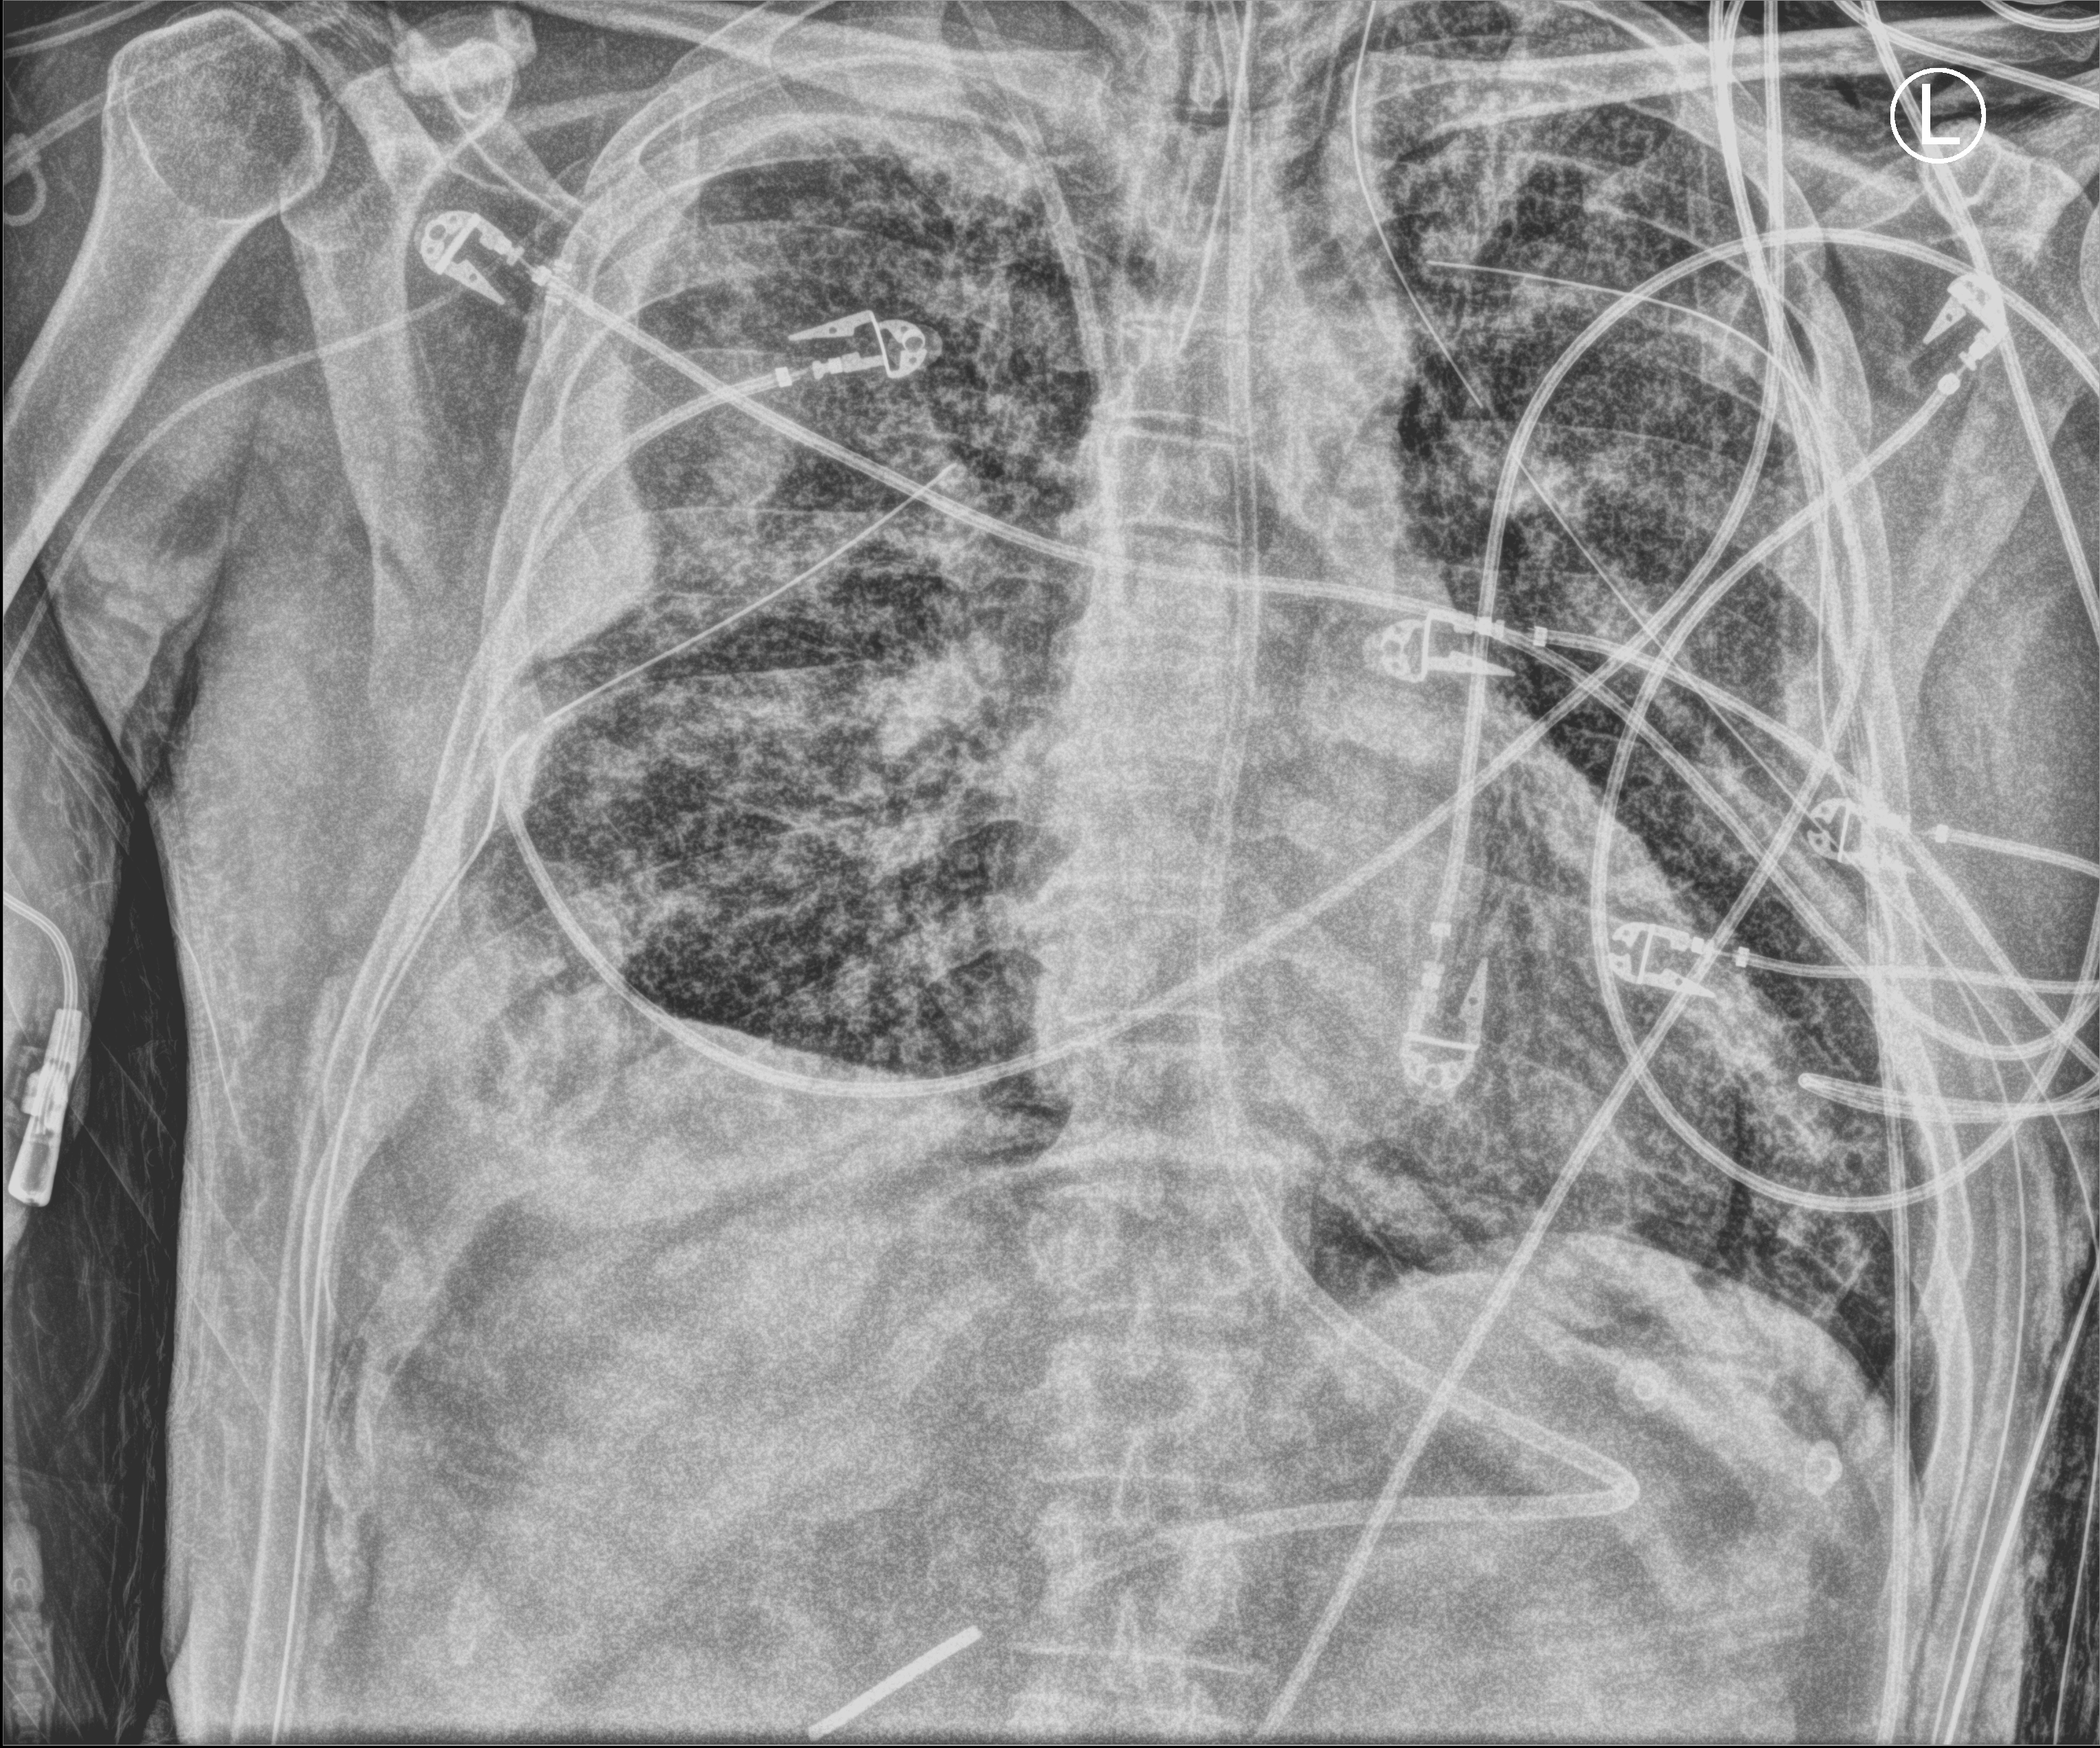
Chest X-ray (portable), anteroposterior (AP) projection. Male patient hospitalised with COVID-19, age 18–59 years.
From the hospital-stay record, not from the radiograph (when in the stay this image was taken is not recorded): COPD (admission record): no.